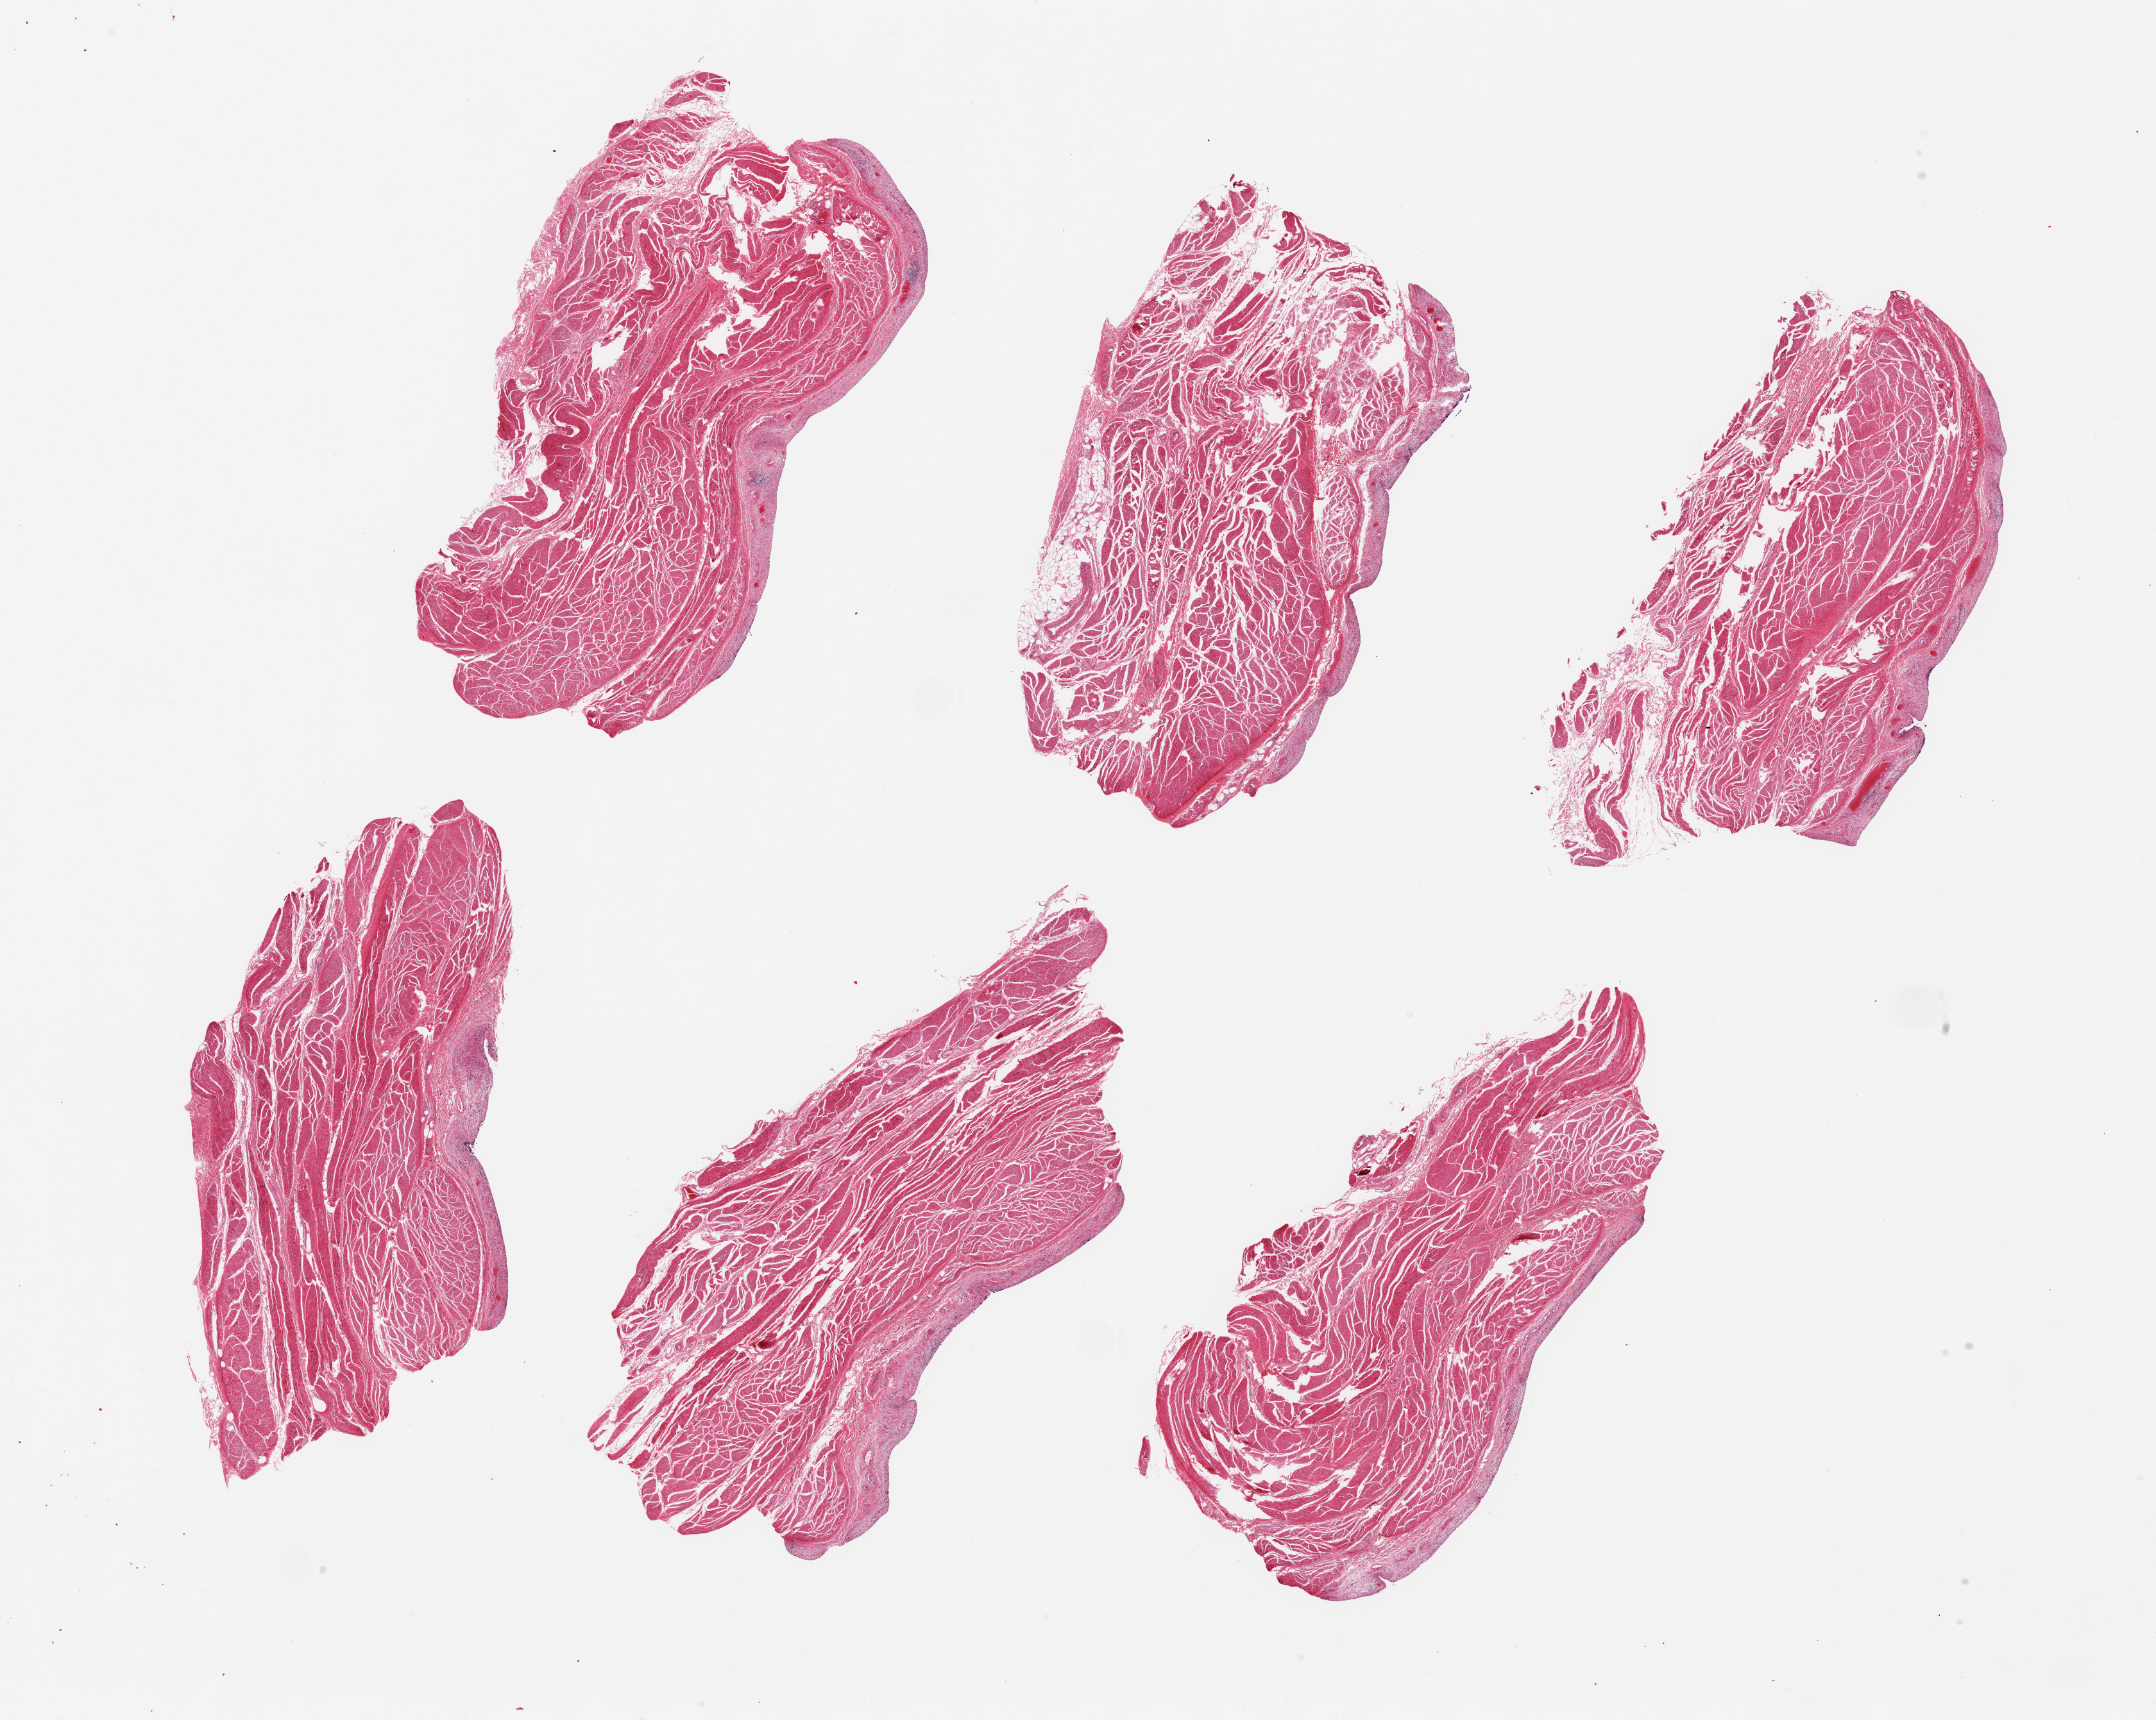
Whole-slide image, H&E stain, a low-resolution overview of the entire scanned area, about 26.6 x 21.2 mm, PAXgene-fixed, paraffin-embedded tissue, target tissue: urinary bladder, donor tissue sample.
Reviewer comment on this tissue sample: 6 pieces ~8x4mm, urothelium completely sloughed.